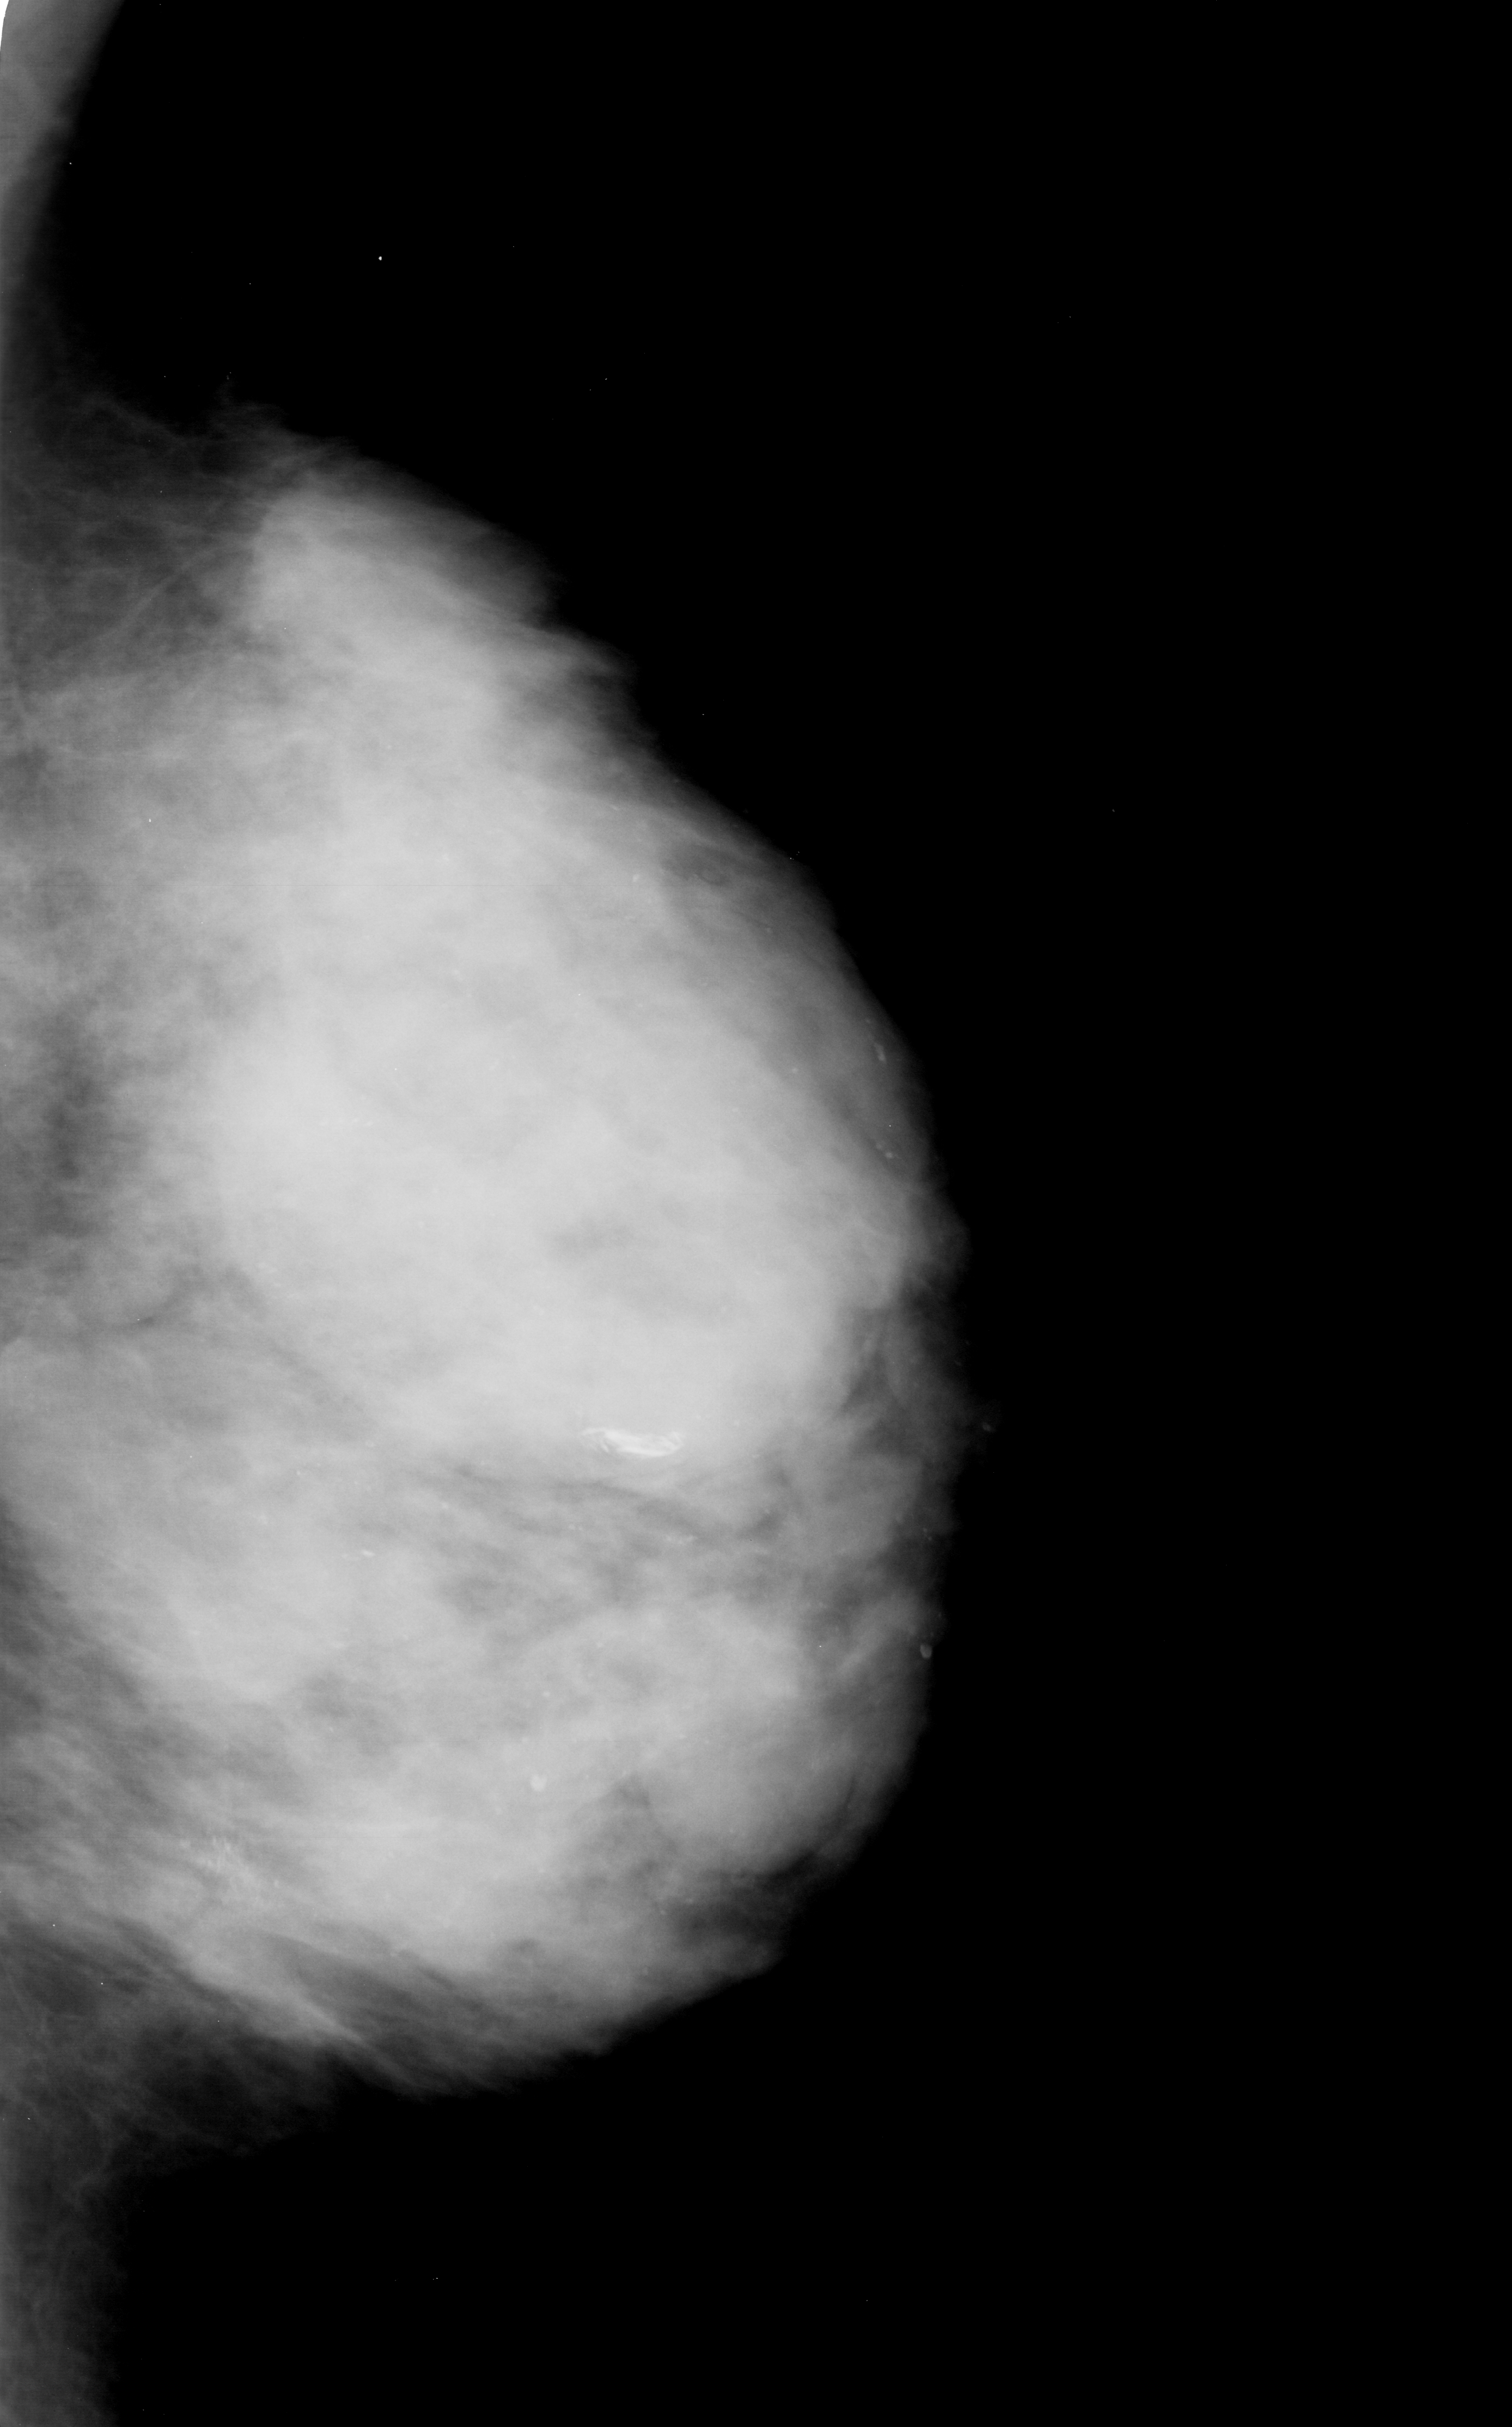
Digitized screen-film mammogram. Left breast. MLO view. BI-RADS breast density category 4 (scale 1–4). 1512 × 2427 image matrix.
Marked abnormalities (boxes around the expert regions of interest):
- mass, shape round, margins circumscribed; BI-RADS assessment category 3; subtlety rating 3 on a 1 (subtle) to 5 (obvious) scale; pathology (as recorded): benign: bounding box <654,1649,850,1883> (left, top, right, bottom; pixels)